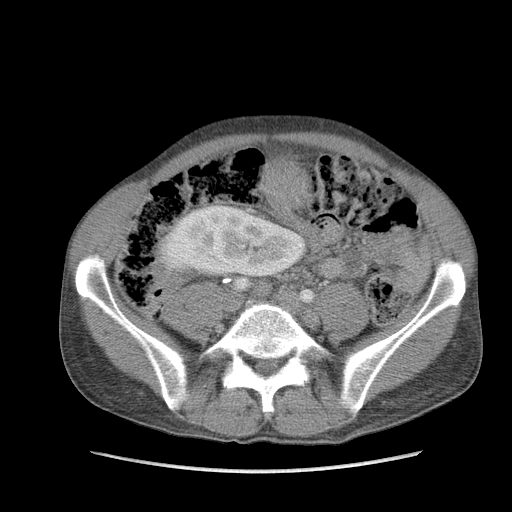
Contrast-enhanced abdominal CT, one axial slice; position 35 of 115 along the scan axis; soft-tissue window (W 400 / L 40 HU); 5 mm slice thickness; 512 × 512 image matrix. Male patient. From the clinical record (not read from this slice): diagnosis: adrenocortical carcinoma; tumour side: right adrenal; Ki-67 index: 13 %.
Annotated regions visible in this slice (semi-automatically segmented with operator editing):
- mass: box from (x=262, y=159) to (x=309, y=210) px